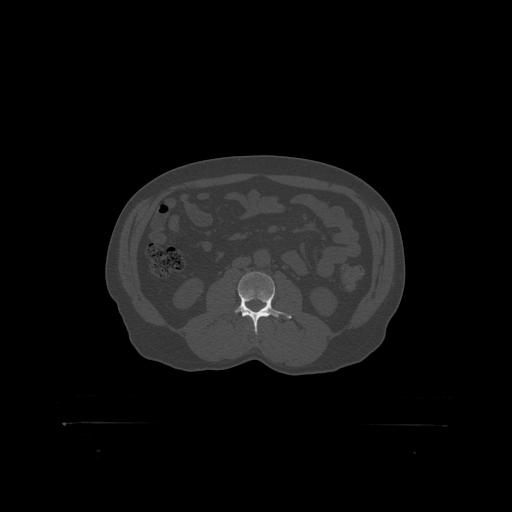
CT including the spine, one axial slice; 120 kVp; bone window (W 1800 / L 400 HU); 1.25 mm slice thickness; 512 × 512 image matrix, field of view 650 × 650 mm. Male patient, age 46 years. Case-level facts recorded for this patient, not image findings: primary cancer: skin.
Outlined on this slice (semi-automatic segmentation, software-assisted and operator-edited):
- L3 vertebra: bounding box (x1, y1, x2, y2) in pixels: (235, 272, 281, 319)